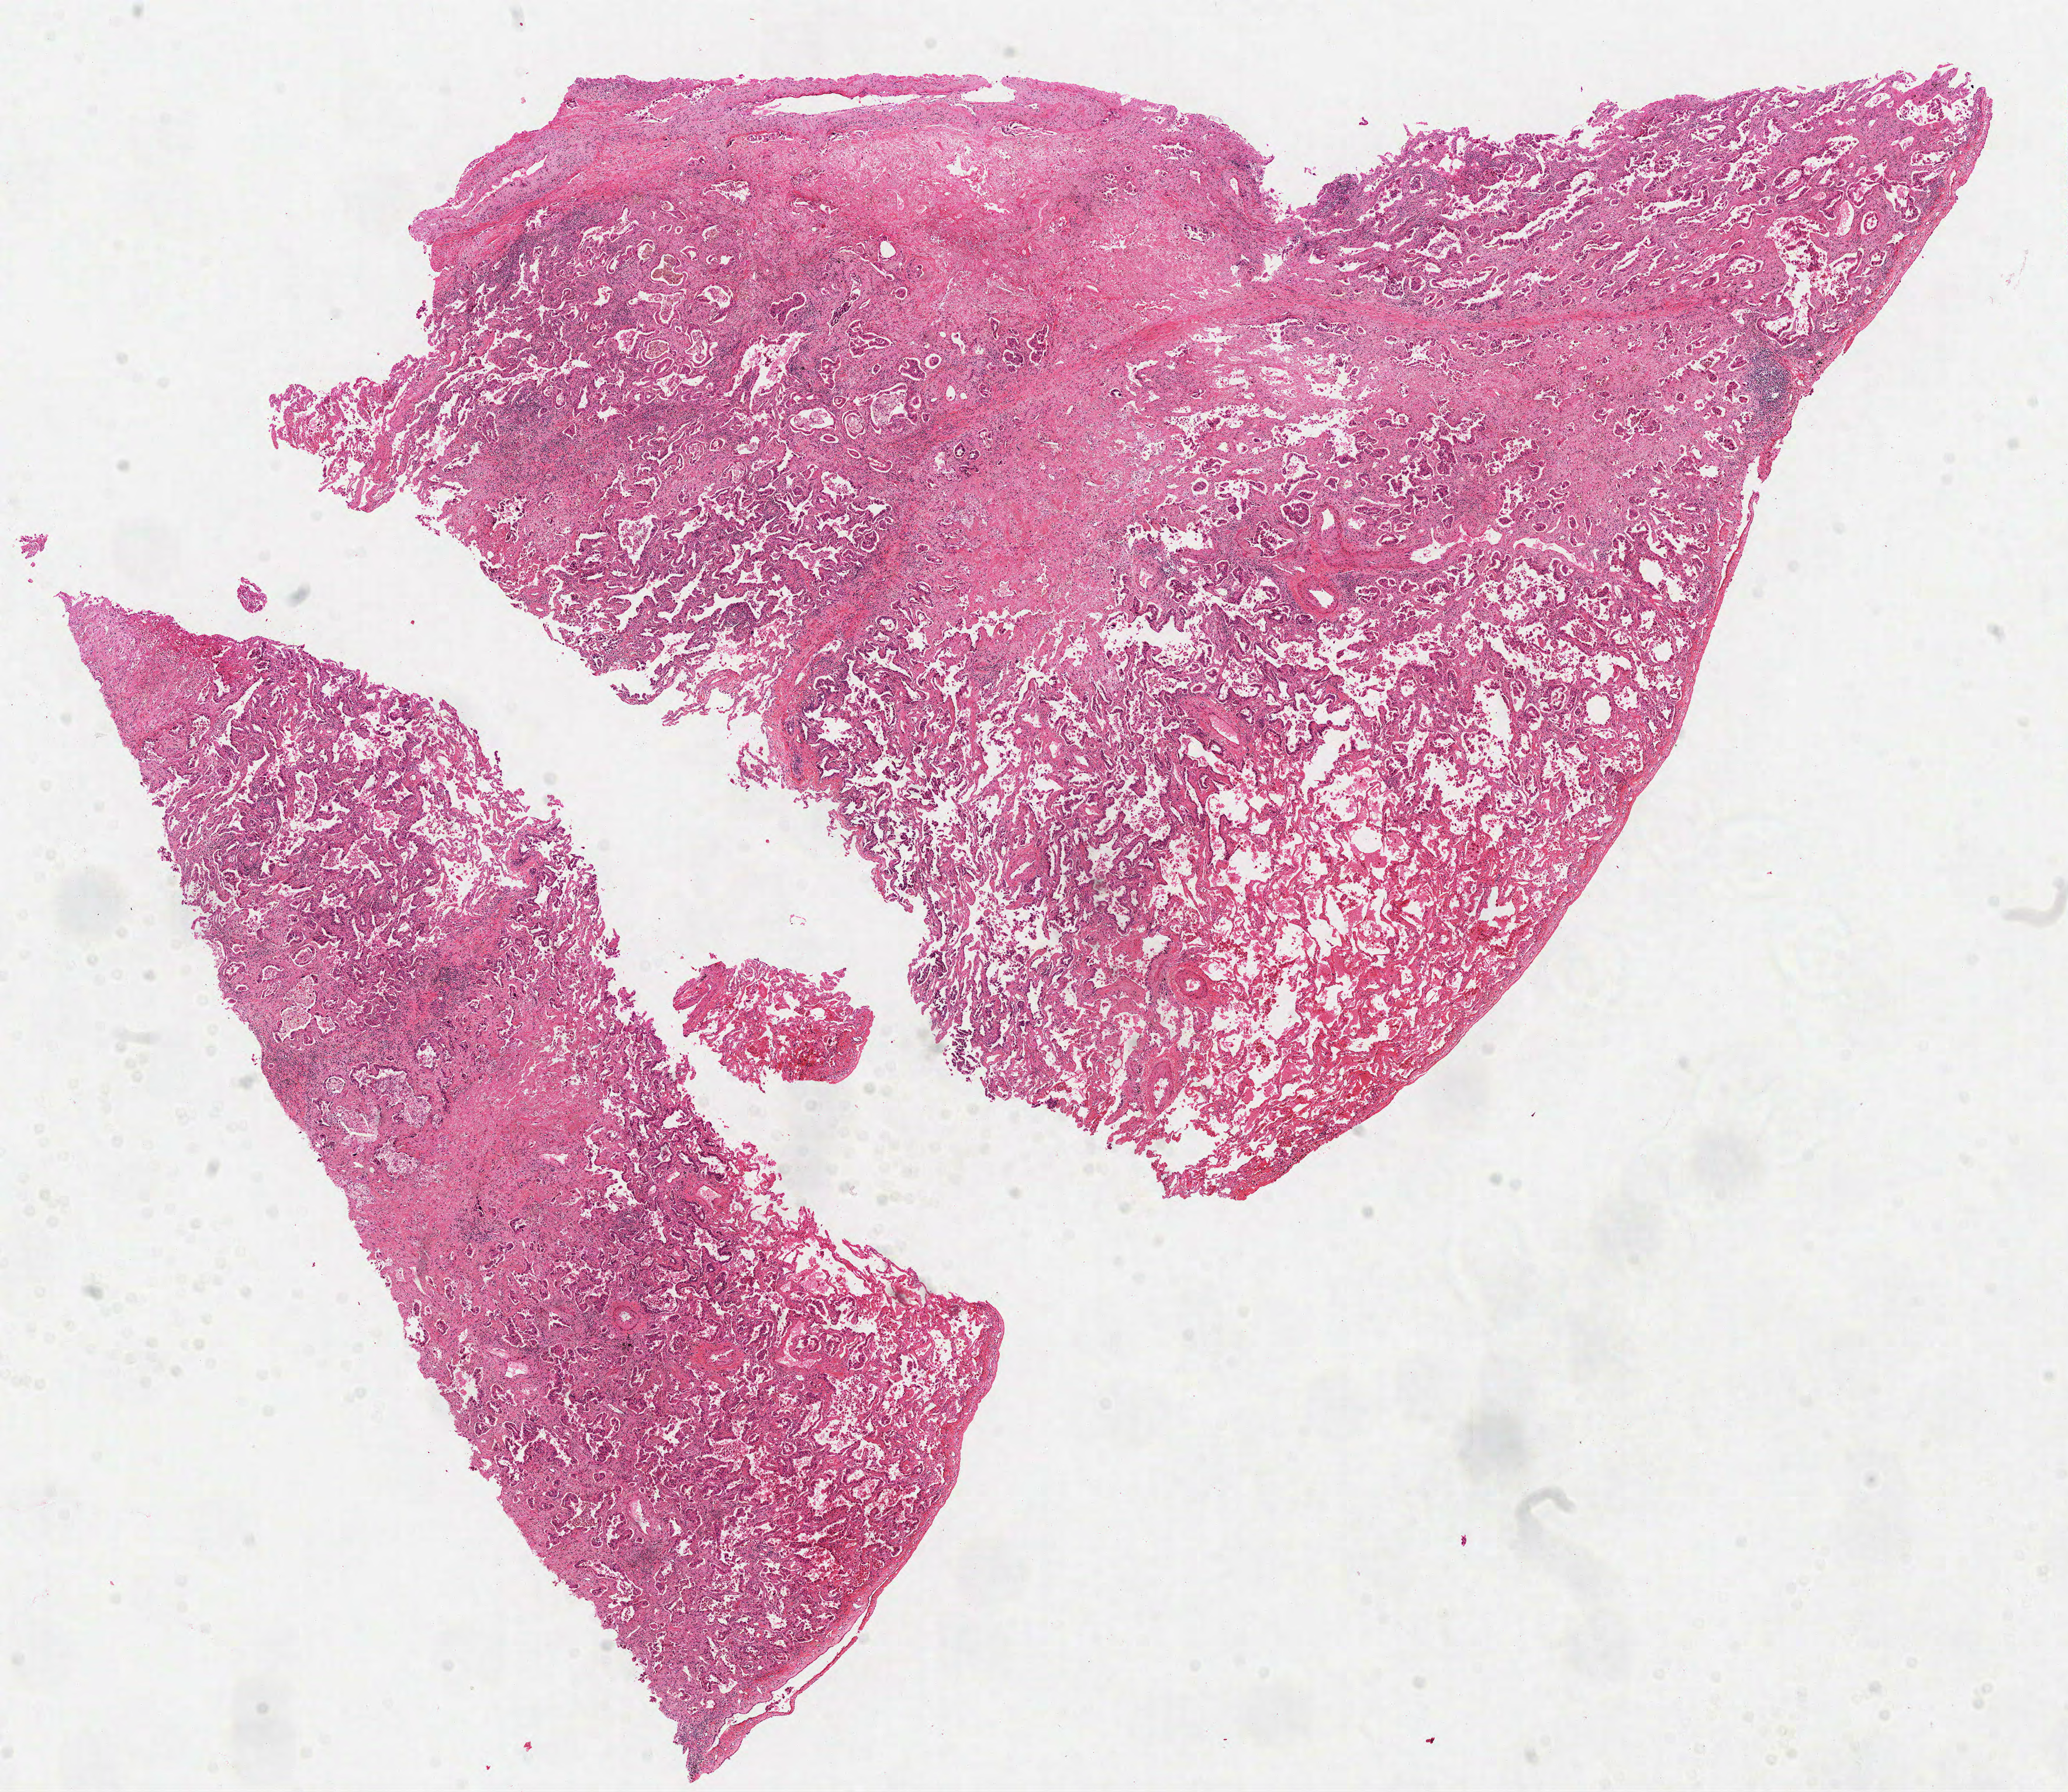
Whole-slide histology image, H&E-stained, low-resolution overview of the scanned area, about 14.3 x 12.4 mm (from a 40x scan), FFPE section, primary tumour sample from the lung. Female patient; age at initial diagnosis 58 years.
• histologic diagnosis: Adenocarcinoma, NOS (upper lobe, lung)
• AJCC pathologic stage: IIIA (6th edition)
• laterality: right